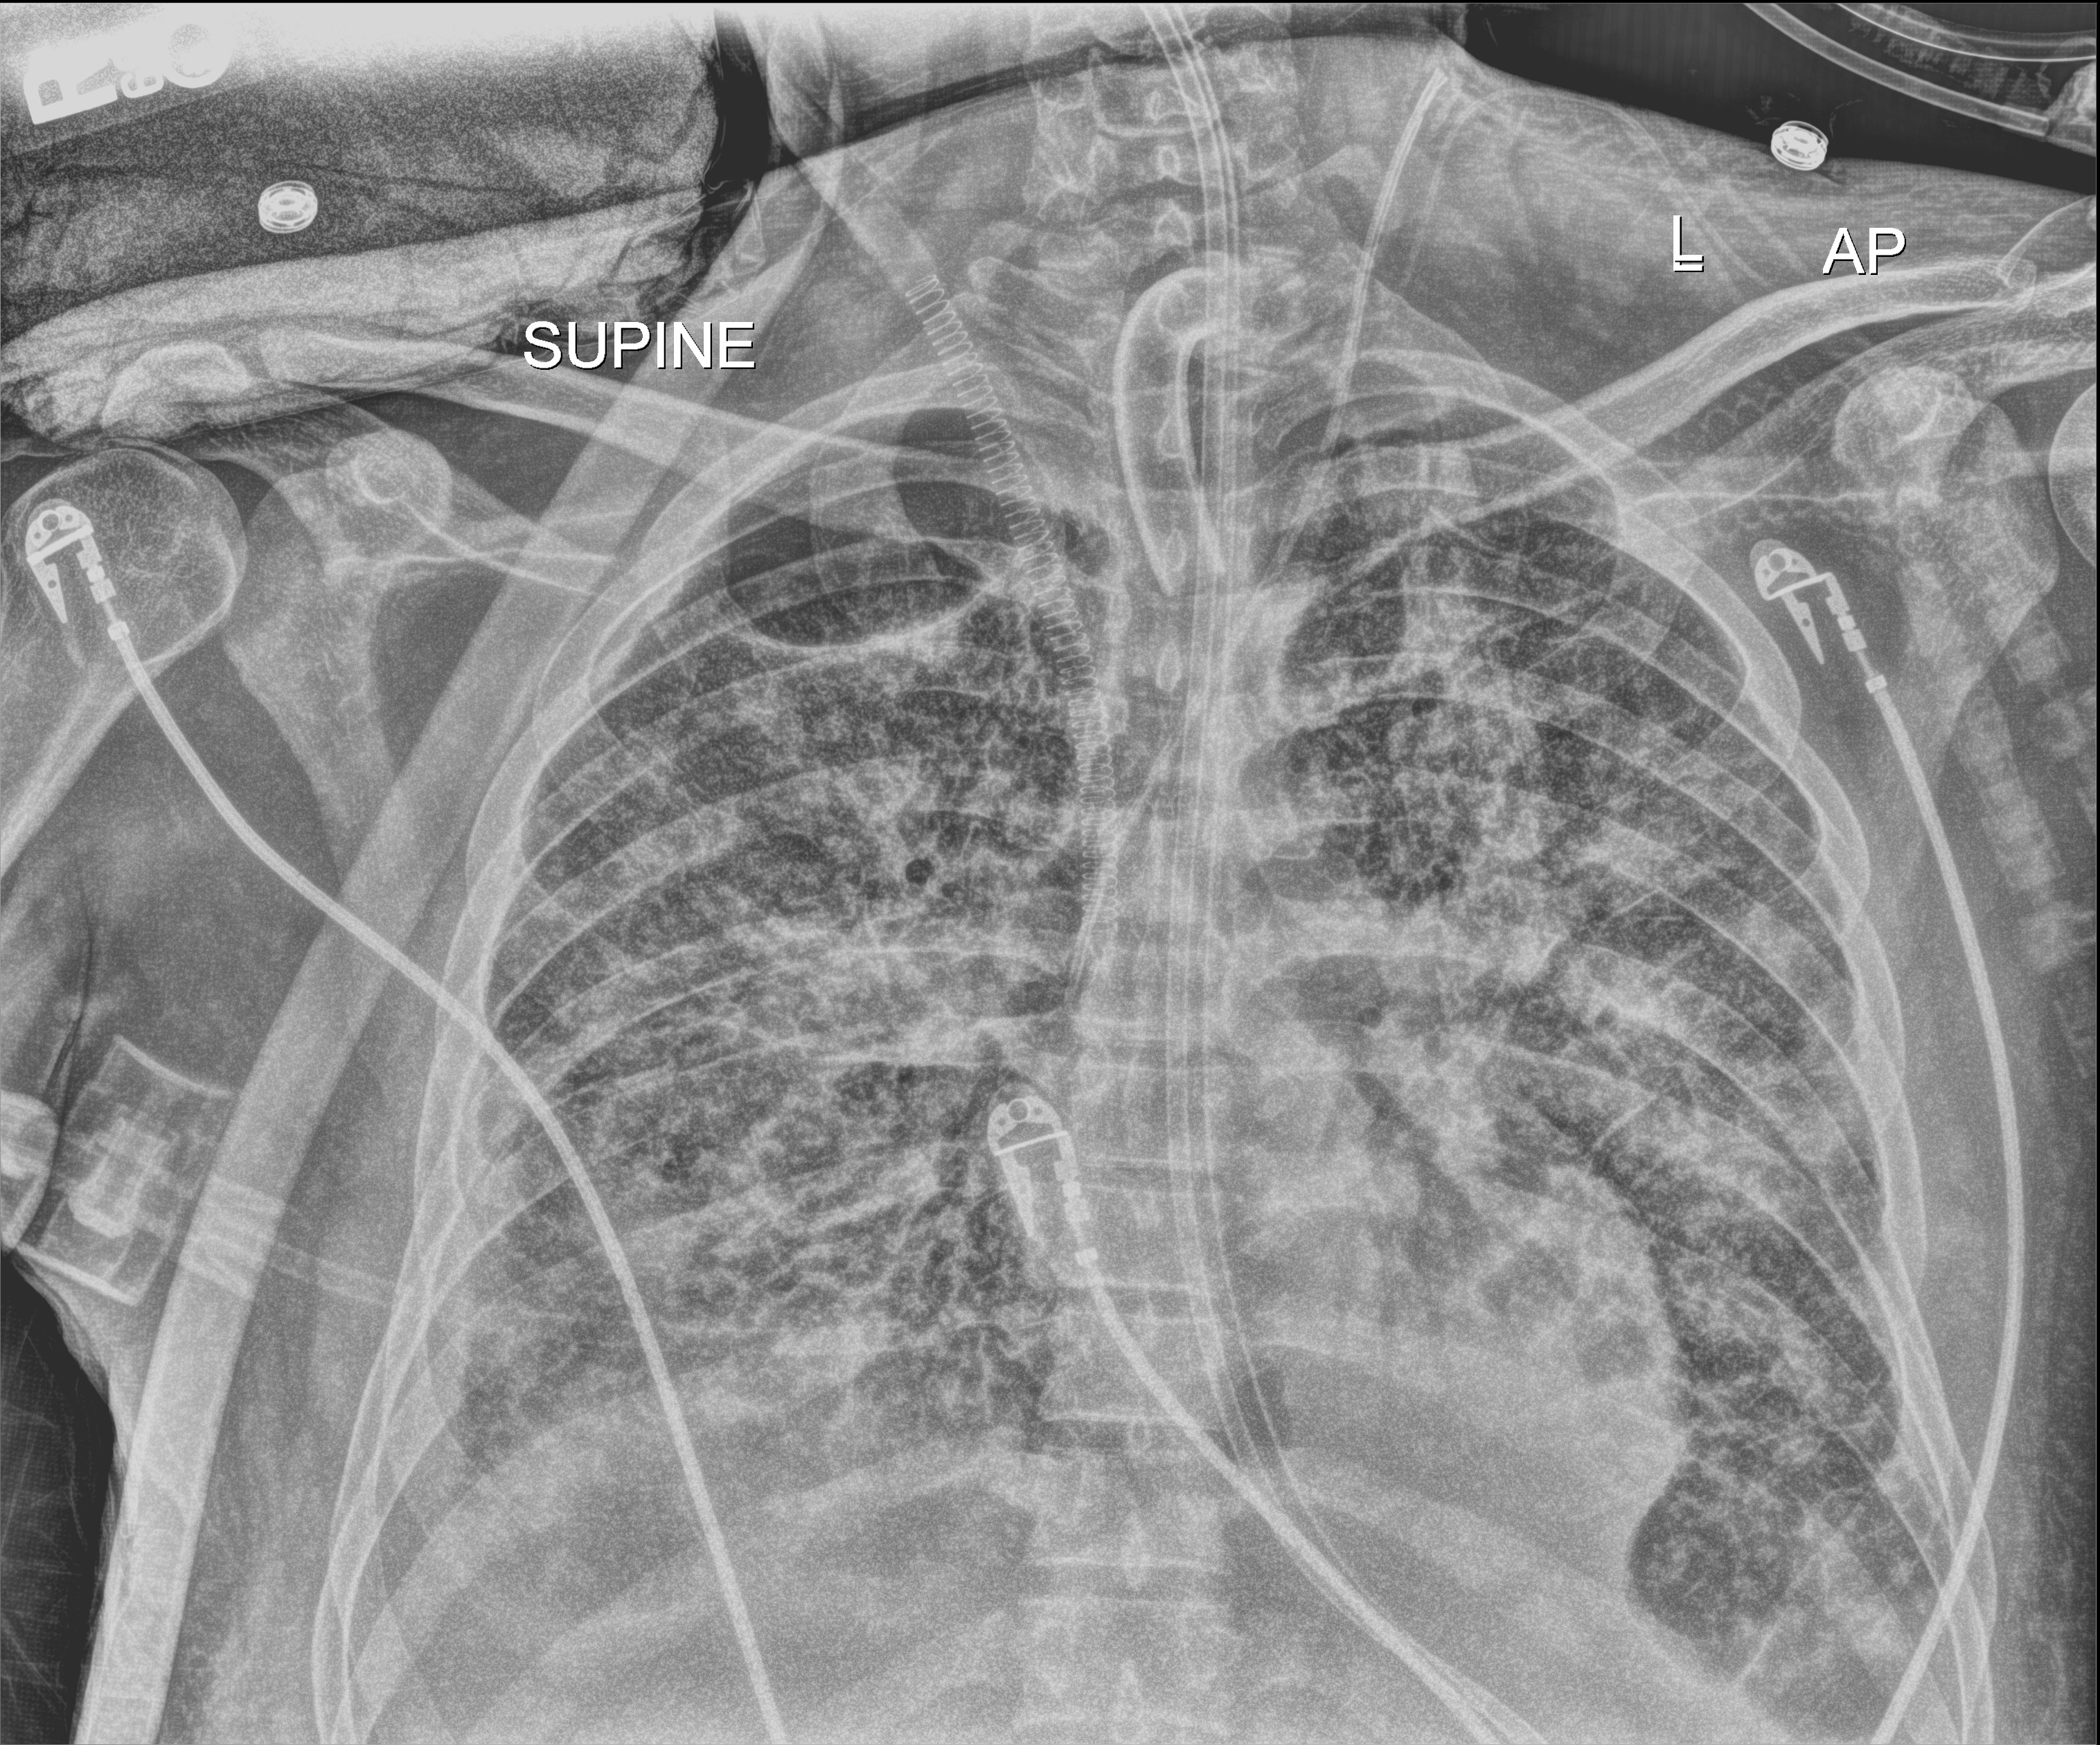
Chest radiograph (digital radiography), anteroposterior (AP) projection. Patient hospitalised with COVID-19, aged 18–59 years.
Admission-level facts for this patient (not findings on this image; timing relative to this image not recorded): mechanically ventilated during this hospital stay: yes; chronic kidney disease (admission record): no.